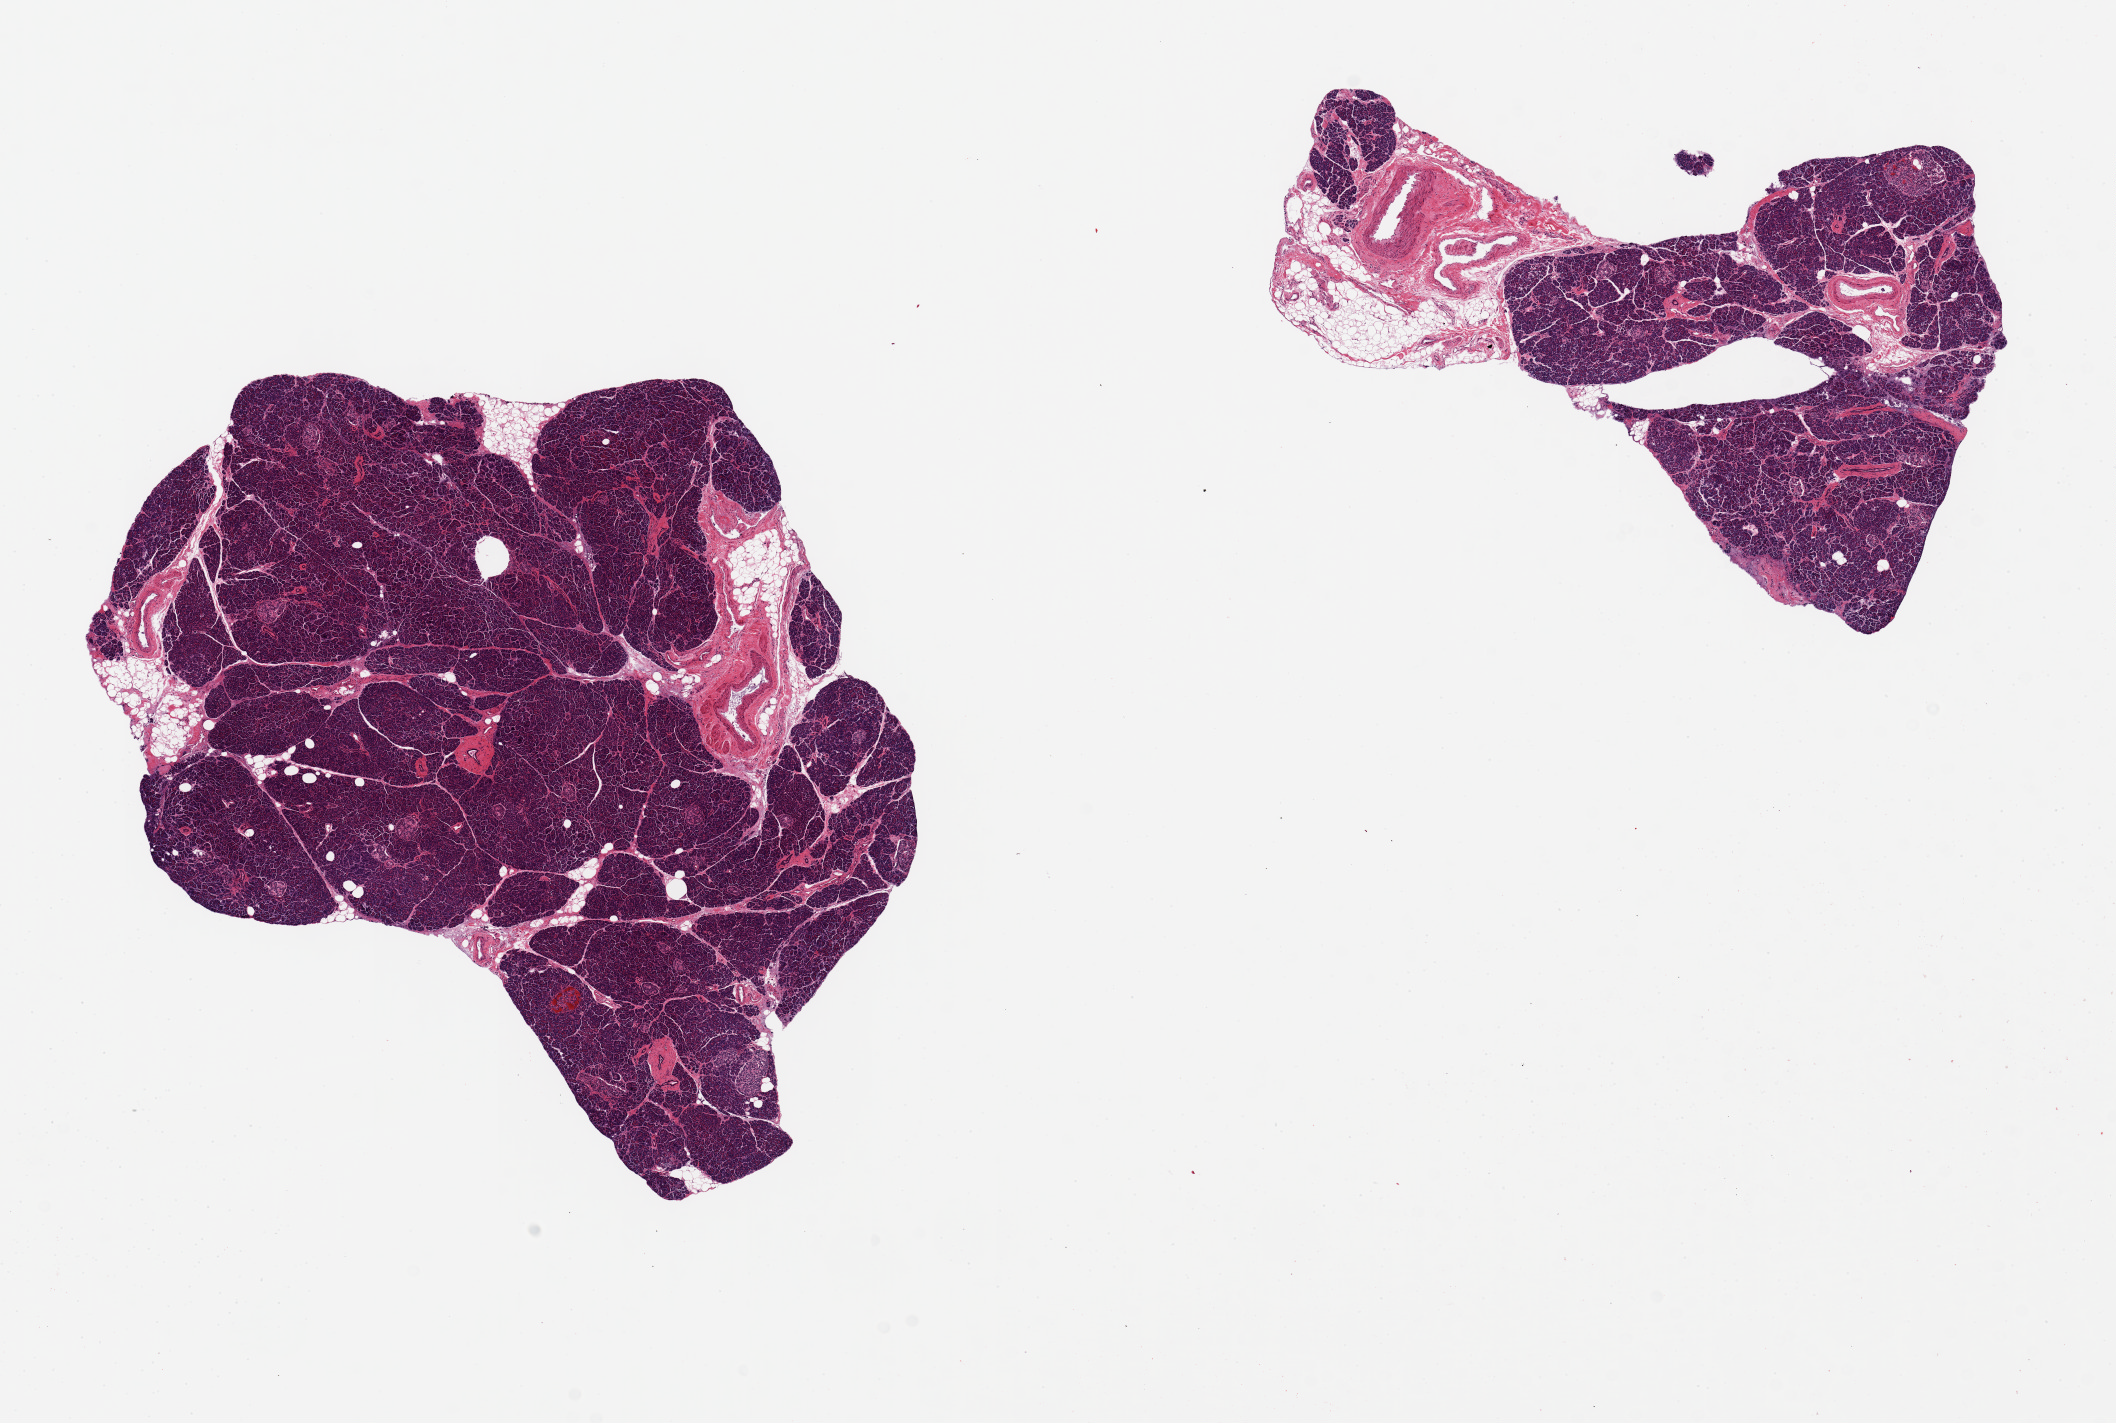
Whole-slide image, haematoxylin and eosin stain — a low-resolution overview of the entire scanned area, about 16.7 x 11.3 mm (slide scanned at 20x). PAXgene-fixed, paraffin-embedded tissue. Target tissue: pancreas. Donor tissue sample. Donor: male.
Reviewer comment on this tissue sample: 2 pieces, 7x6 & 6x4mm; 1 with 30% peripheral adipose & vascular tissue.